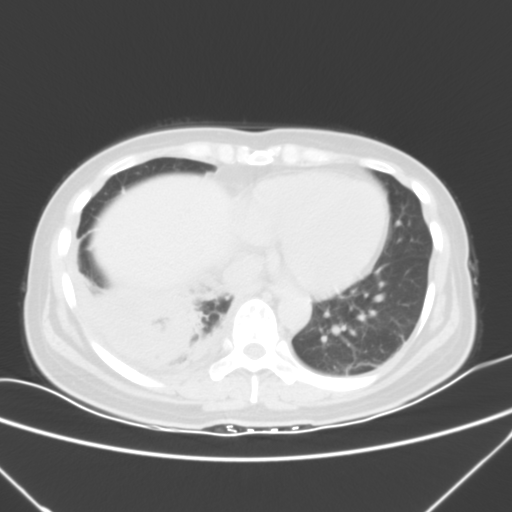
Chest CT, one axial slice; slice 14 of 53 in the series (ordered by position); lung window (W 1500 / L -600 HU); 512 × 512 image matrix, field of view 337 × 337 mm. Female patient, age 42 years. Case-level facts recorded for this patient, not image findings: clinical TNM (as recorded): T3 N0 M1c.
Annotated regions visible in this slice (bounding box drawn by a radiologist):
- lung tumour (recorded histology: adenocarcinoma): bounding box (x1, y1, x2, y2) in pixels: (86, 275, 201, 378)